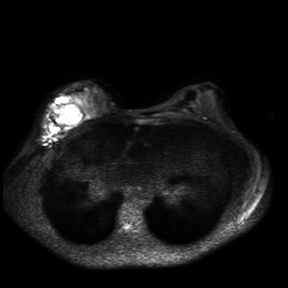
Breast MRI, one axial slice. Position 21 of 30 along the scan axis. Diffusion-weighted series; image 2 of 4 stored at this slice position (different b-values; order by instance number). 3 T. 288 × 288 image matrix, field of view 360 × 360 mm. Female patient.
Annotated regions visible in this slice (expert manual segmentation):
- tumour on diffusion-weighted imaging: bounding box [x1, y1, x2, y2] px = [55, 97, 67, 123]